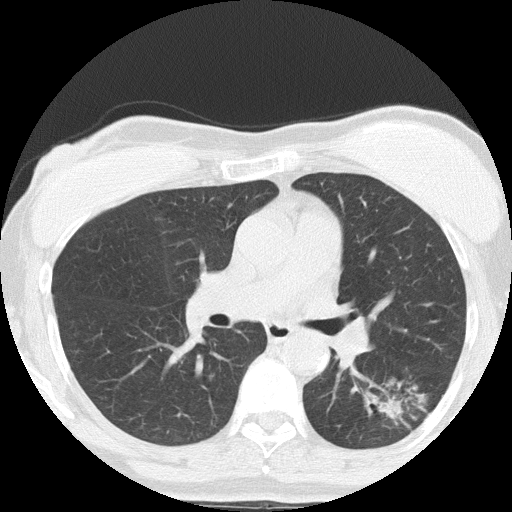
Axial slice from a low-dose chest CT screening exam. Third screening round (two years after baseline). Lung window (W 1500 / L -600 HU). 2 mm slice thickness. Lung (sharp) reconstruction kernel (FC51). Slice 67 of 152 in the series. Female, age 64 years at enrolment. Former smoker at enrolment.
• Lesion marked by an expert reader, bounding box <361,370,450,444> (left, top, right, bottom; pixels).
• The screening reader recorded 3 non-calcified nodules or masses ≥4 mm on this exam (right upper lobe, left lower lobe, right middle lobe); which of them this box marks is not recorded.
• Official screen result: positive, other.
• Lung cancer was diagnosed 212 days after this screen: adenocarcinoma, NOS, left lower lobe, moderately differentiated (G2), stage IA (AJCC 6th edition), 17 mm at pathology.